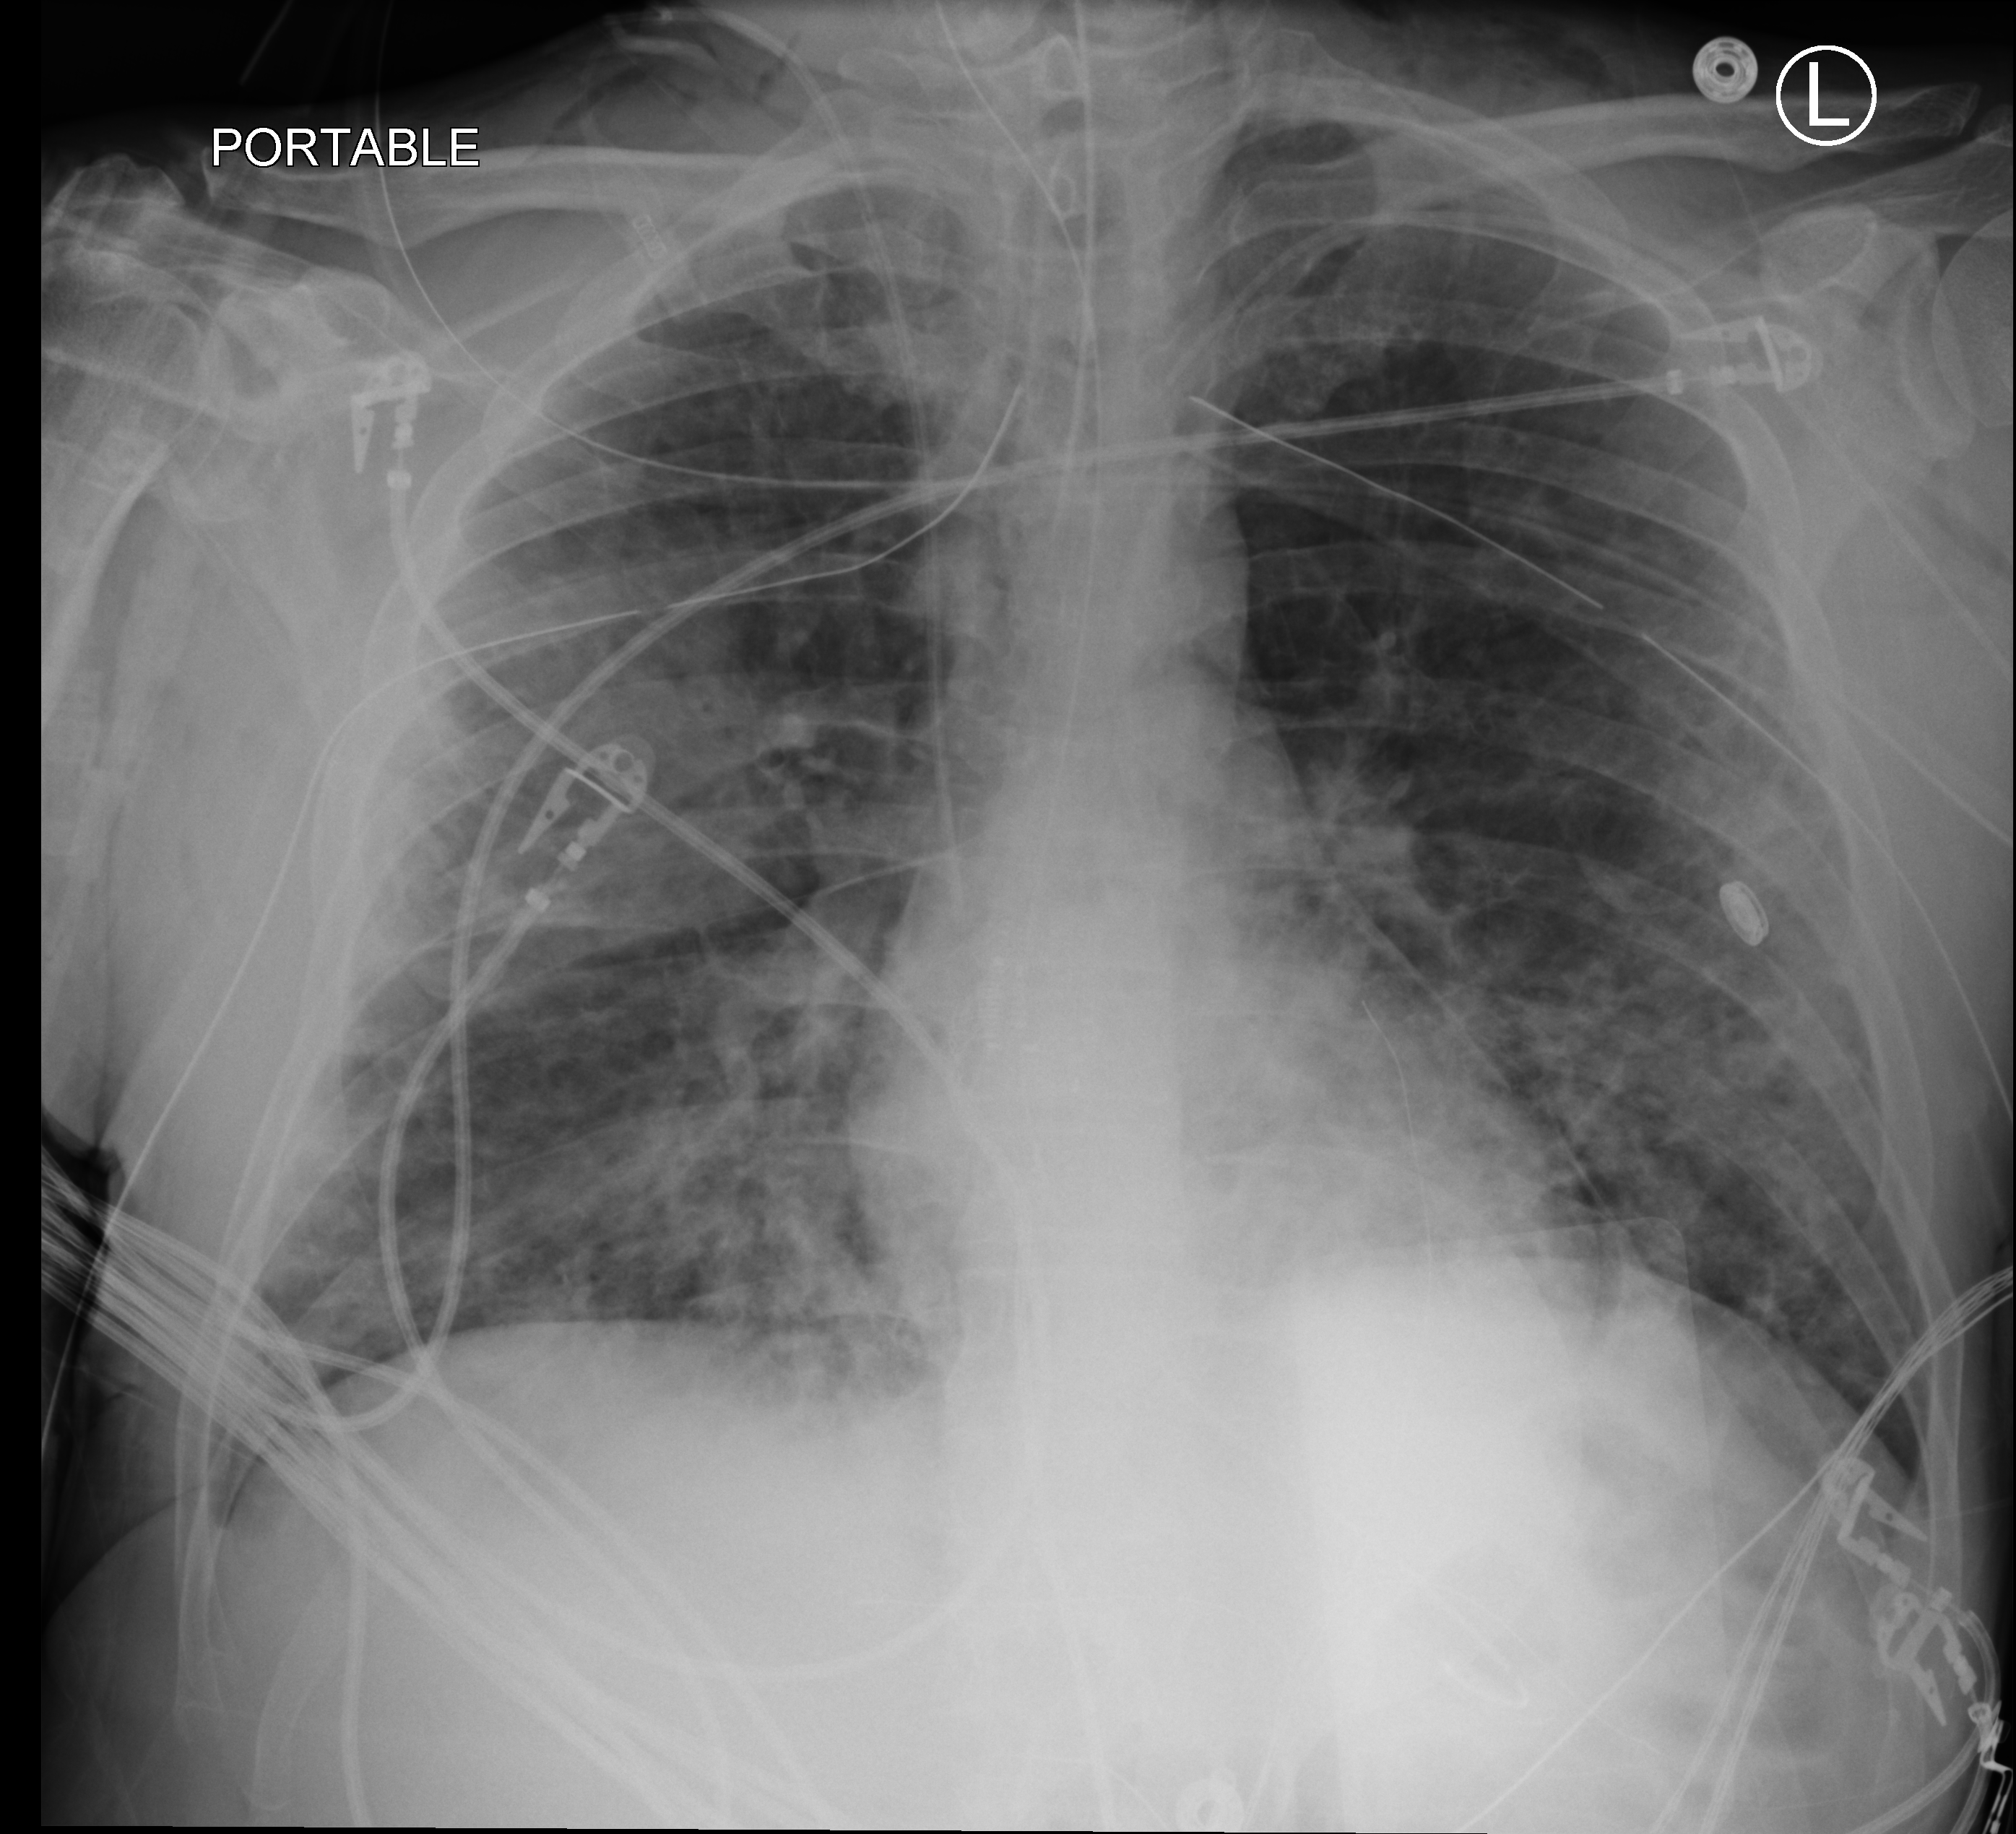
Chest X-ray (portable). Male patient hospitalised with COVID-19, age 18–59 years.
Hospital-stay facts (about this admission, not read from this image; timing relative to this image not recorded): chronic kidney disease (admission record): no.